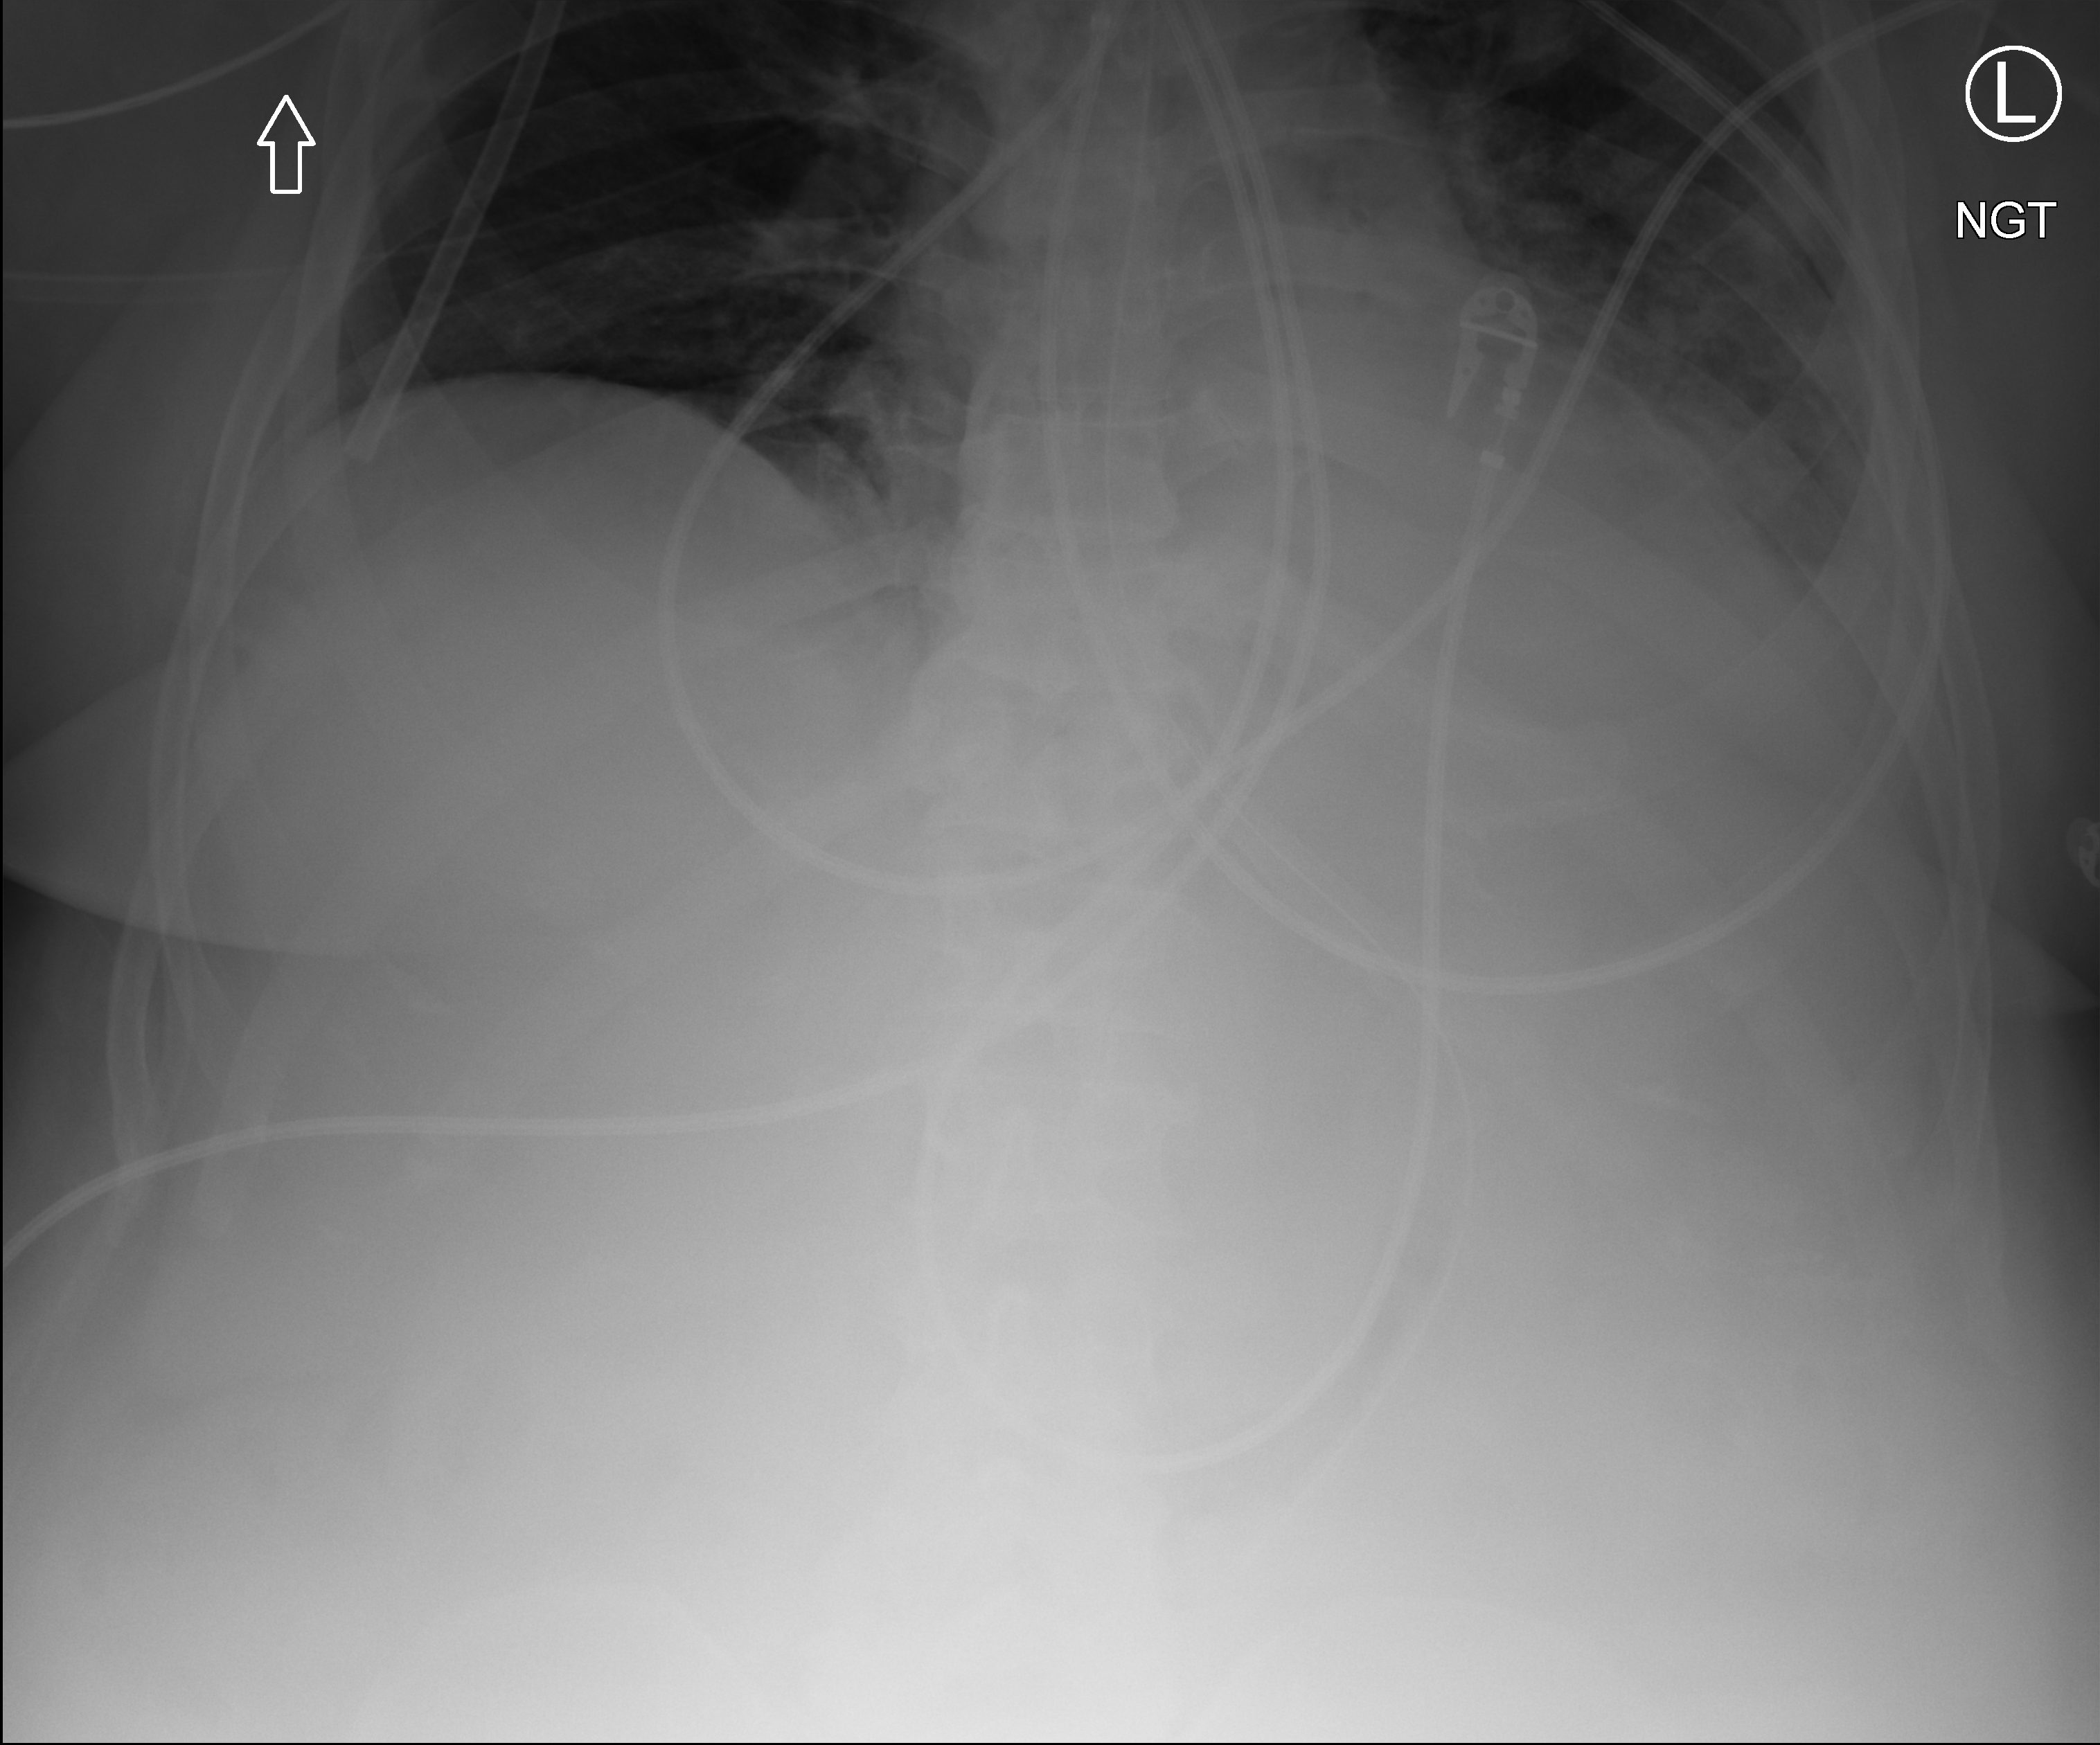
Abdomen X-ray (portable), anteroposterior (AP) projection. Patient hospitalised with COVID-19; male, aged 60–74 years.
Admission-level facts for this patient (not findings on this image; timing relative to this image not recorded):
- admitted to intensive care during this hospital stay: yes
- diabetes (admission record): yes